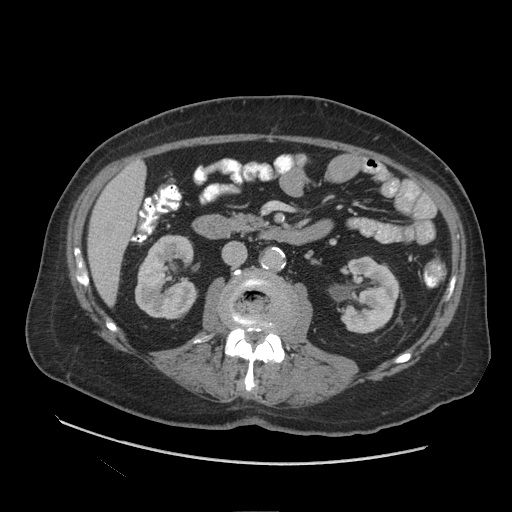
Contrast-enhanced abdominal CT (liver protocol), one axial slice. Position 31 of 109 along the scan axis. Reconstruction kernel STANDARD. 140 kVp. Soft-tissue window (W 400 / L 40 HU). 512 × 512 image matrix, field of view 420 × 420 mm. Case-level facts recorded for this patient, not image findings: diagnosis: hepatocellular carcinoma (patient treated with transarterial chemoembolisation; whether this scan precedes or follows treatment is not stated here); TNM stage (as recorded): Stage-I; Child-Pugh class: A; tumour nodularity: uninodular.
Annotated regions visible in this slice (semi-automatically segmented with operator editing):
- liver parenchyma outside the tumour (the mass and vessels are separate outlines, so this box may not span the whole liver): box from (x=88, y=161) to (x=144, y=306) px
- liver vessels: (x=121, y=222)–(x=123, y=224)